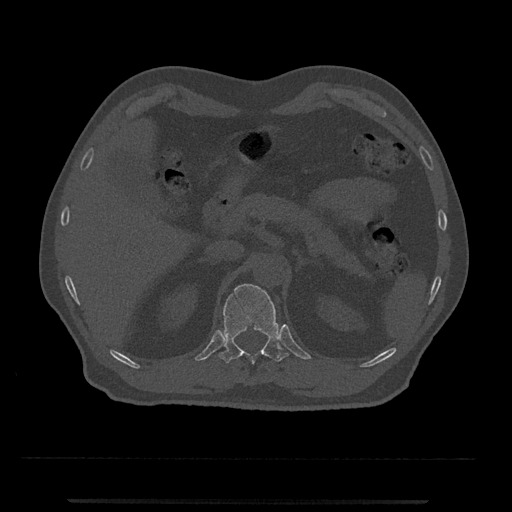
CT including the spine, one axial slice; slice 409 of 797 in the series (ordered by position); bone window (W 1800 / L 400 HU); 0.5 mm slice thickness; 512 × 512 image matrix, field of view 419 × 419 mm. Male patient, age 63 years. From the clinical record (not read from this slice): primary cancer: prostate.
Annotated regions visible in this slice (semi-automatic segmentation, software-assisted and operator-edited):
- T12 vertebra: bounding box (x1, y1, x2, y2) in pixels: (218, 283, 289, 364)